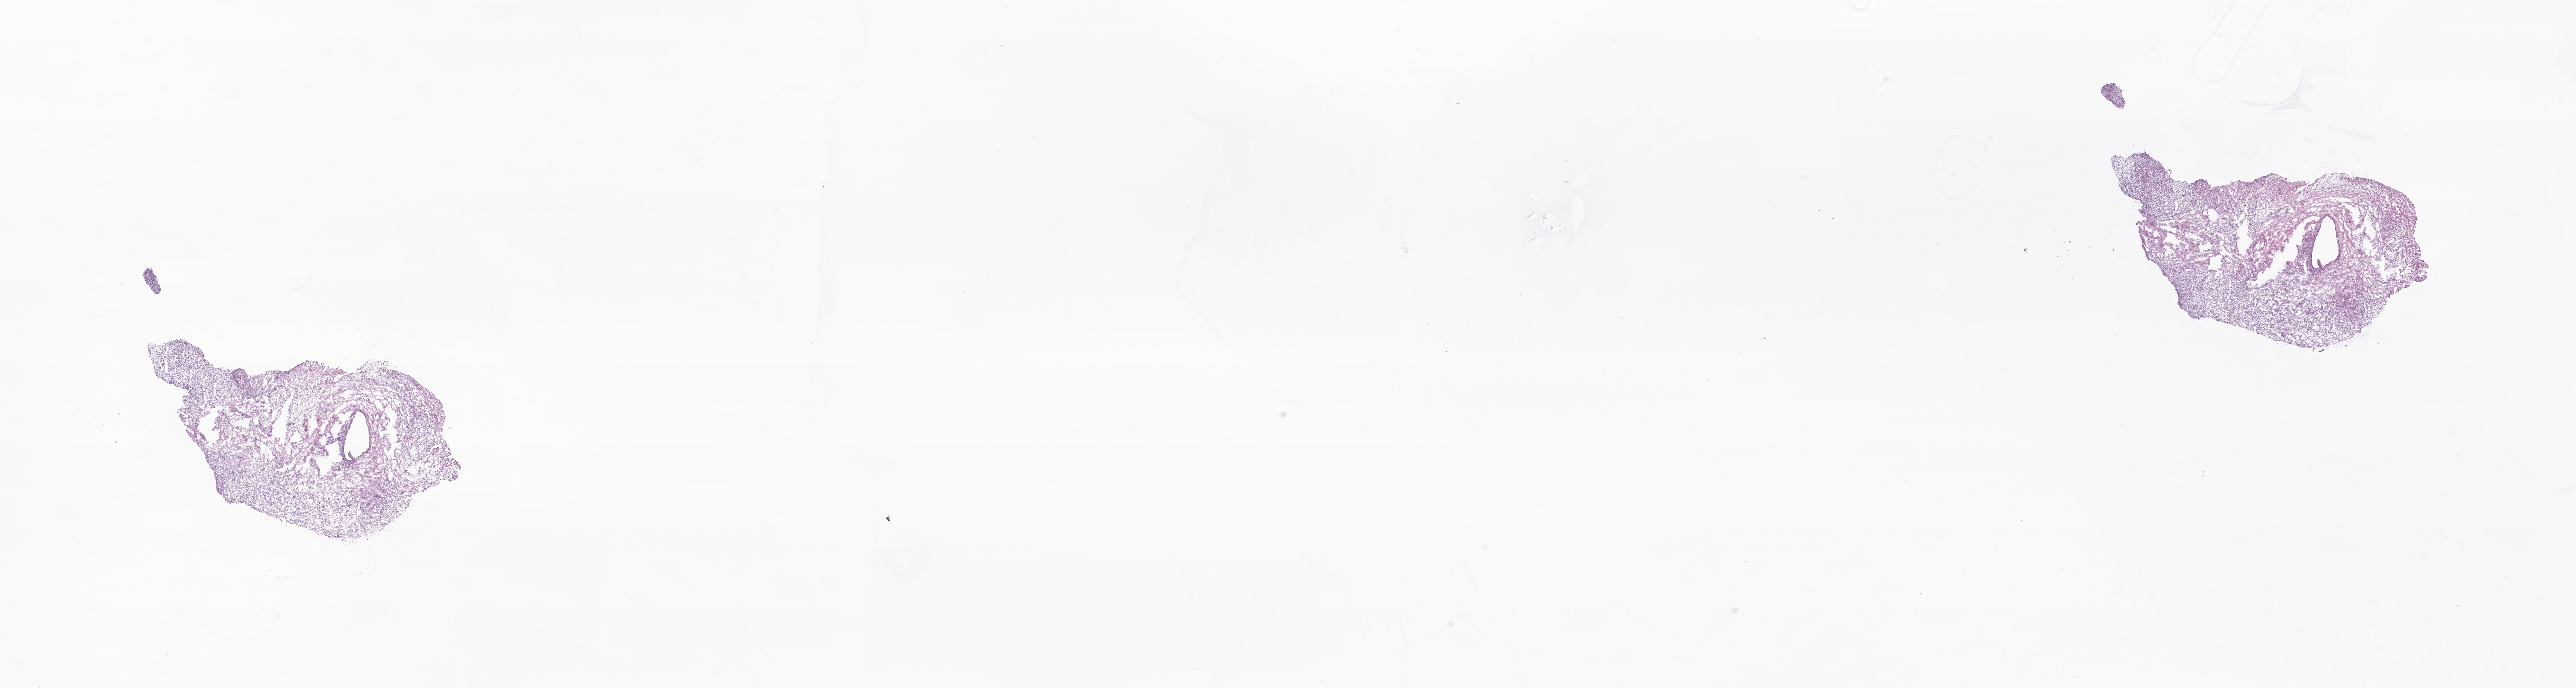
Whole-slide image, H&E stain of tumor tissue from the pelvis — a low-resolution overview of the entire scanned area, about 33.8 x 9.0 mm; cryosection (OCT / tissue freezing medium). Patient: female, age 39 months (3 years 3 months).
* diagnosis (ICD-O-3 morphology term): Embryonal rhabdomyosarcoma, NOS